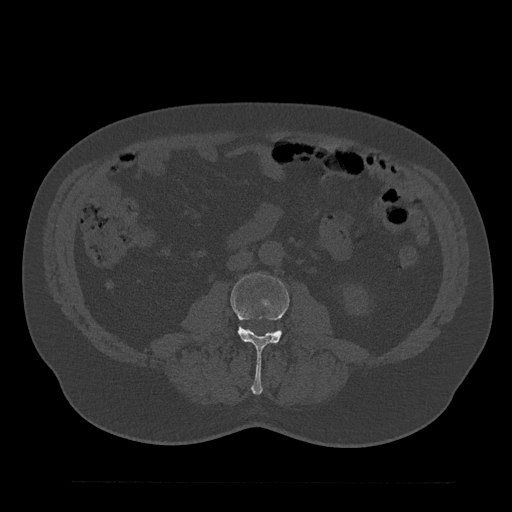
CT including the spine, one axial slice; slice 26 of 797 in the series (ordered by position); 120 kVp; bone window (W 1800 / L 400 HU); 0.5 mm slice thickness; 512 × 512 image matrix, field of view 430 × 430 mm. Patient: male, 61 years. Case-level facts recorded for this patient, not image findings: primary cancer: prostate.
Outlined on this slice (semi-automatically segmented with operator editing):
- L3 vertebra: box from (x=231, y=273) to (x=289, y=394) px